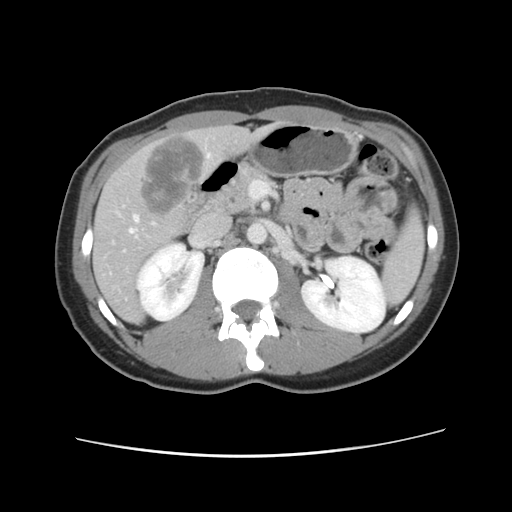
Contrast-enhanced abdominal CT, one axial slice; position 47 of 134 along the scan axis; intravenous contrast given; soft-tissue window (W 400 / L 40 HU); 2.5 mm slice thickness; 512 × 512 image matrix, field of view 339 × 339 mm. Female patient, age 33 years. From the clinical record (not read from this slice): diagnosis: colorectal cancer liver metastases, imaged before liver resection; multiple liver metastases: yes; largest metastasis: 4.5 cm; chemotherapy before resection: no.
Outlined on this slice (expert manual segmentation):
- hepatic veins: bounding box [x1, y1, x2, y2] px = [129, 154, 210, 233]
- liver: [94, 126, 271, 322]
- planned liver remnant (the part of the liver to remain after resection): [93, 128, 273, 322]
- liver metastasis: [138, 135, 205, 218]